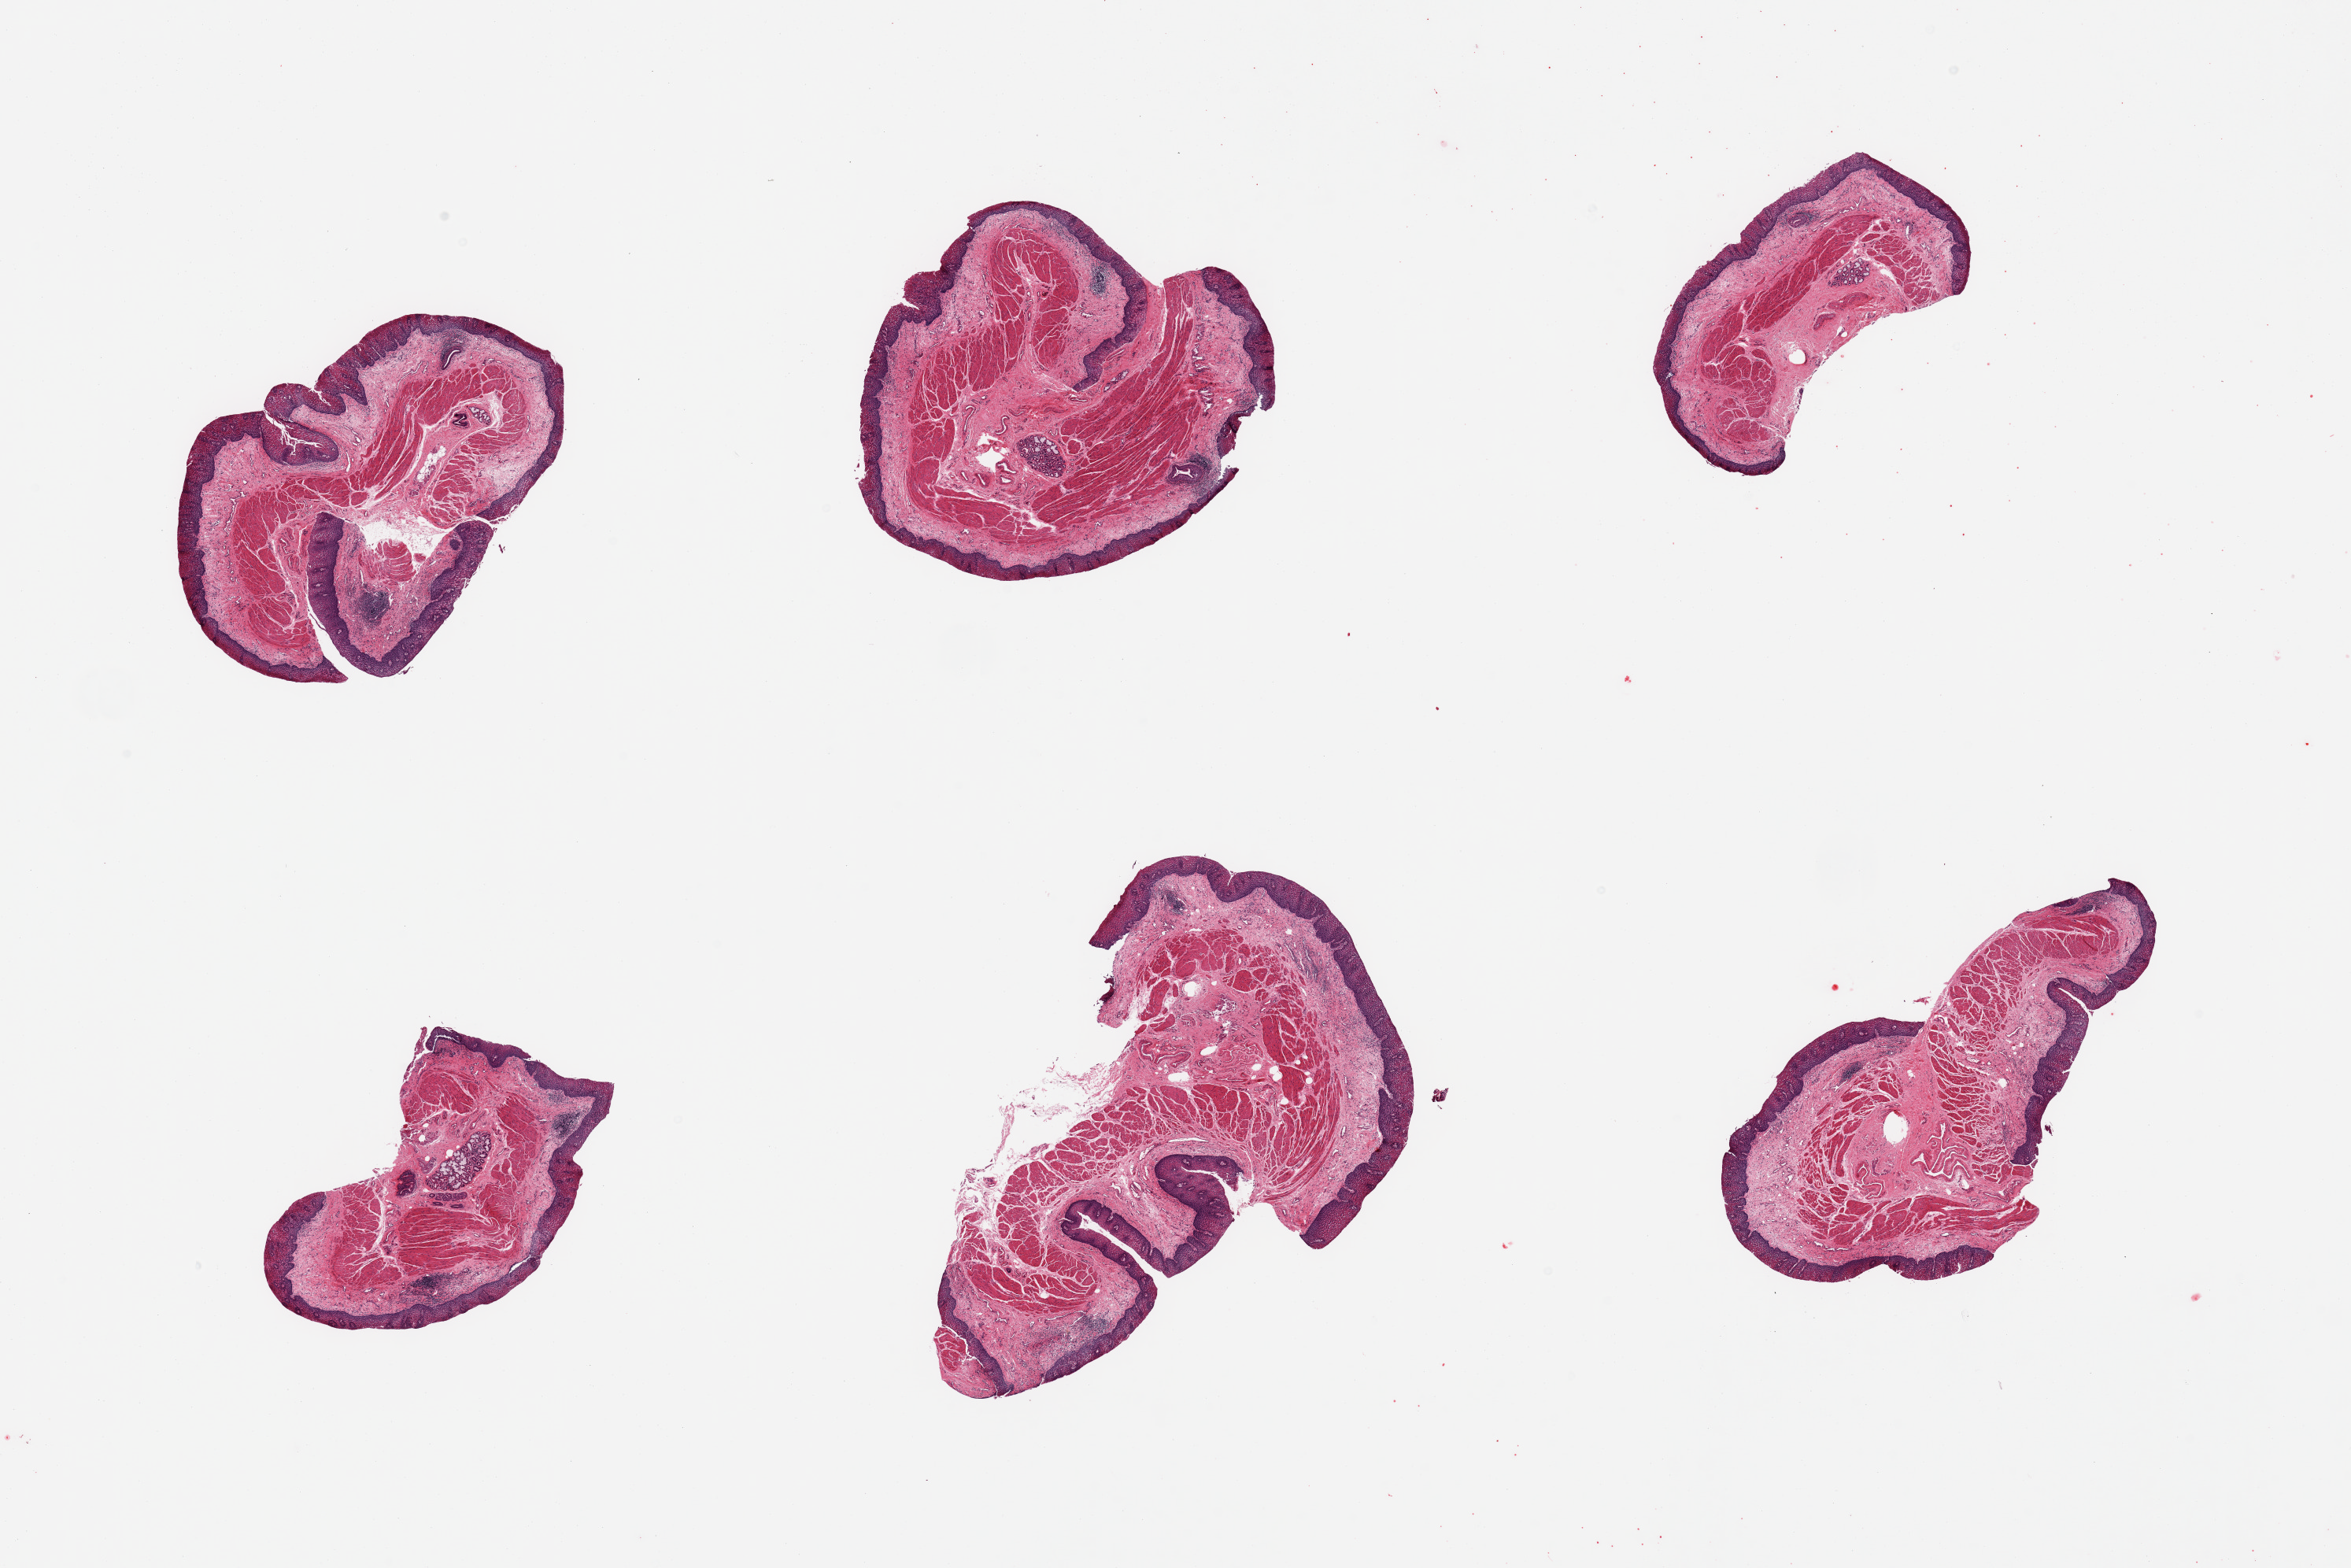
Digitized hematoxylin and eosin (H&E)-stained section, a low-resolution overview of the entire scanned area, about 23.6 x 15.8 mm (from a 20x scan), PAXgene-fixed paraffin-embedded (PFPE) section, target tissue: esophageal mucous membrane, tissue donor sample. Donor sex: male.
Reviewer comment on this tissue sample: 6 pieces, squamous mucosa up to ~0.25mm, ~15% thickness.